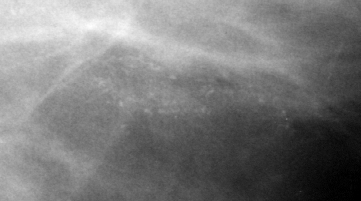
Region of interest cut from a scanned film mammogram (one marked finding); left breast; MLO view.
Marked abnormality: calcifications, morphology fine linear branching, distribution clustered / linear; BI-RADS assessment category 4; pathology result (as recorded, not read from the image): benign.